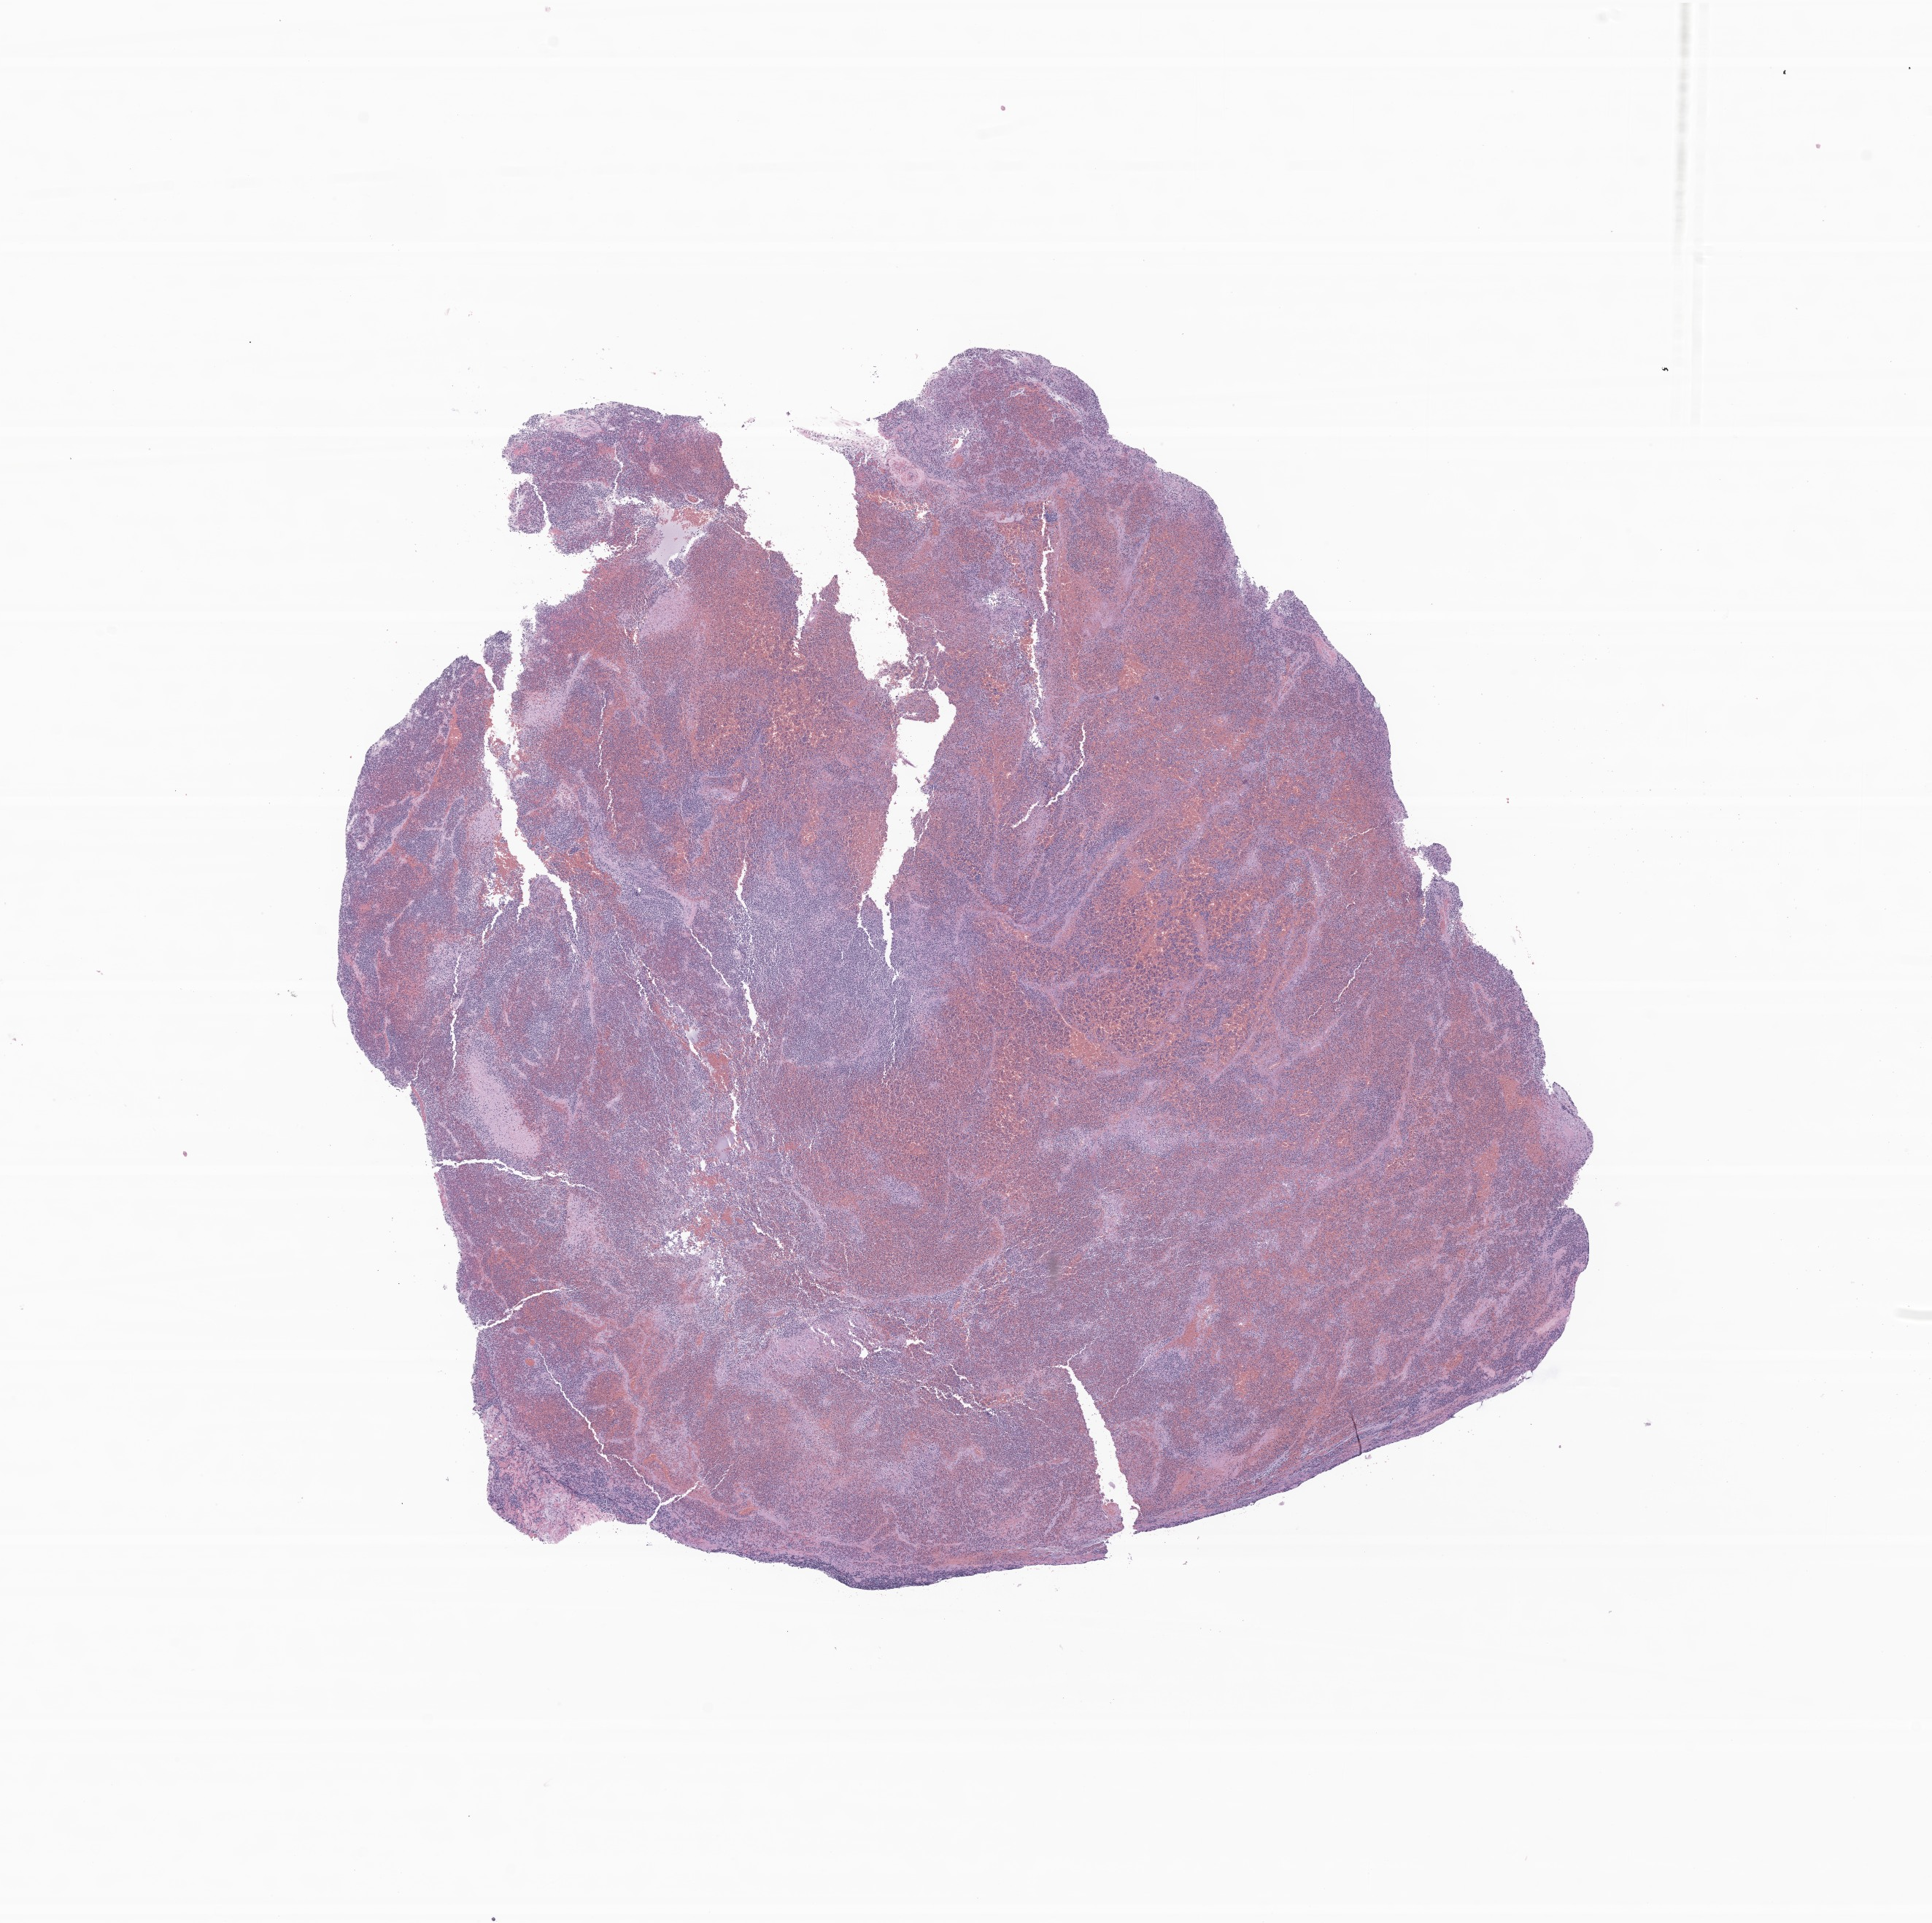
Digitized H&E-stained section of tumor tissue from the abdomen — a low-resolution overview of the entire scanned area, about 11.2 x 11.1 mm. Formalin-fixed, paraffin-embedded (FFPE) tissue. Male patient, age 751 days (about 2.1 years).
Recorded diagnosis: Neuroblastoma, NOS.